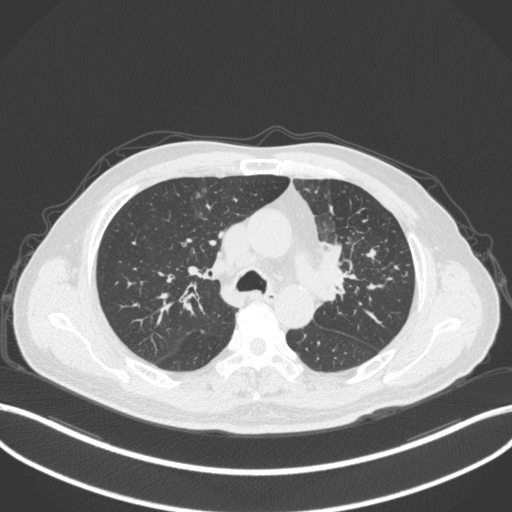
Chest CT, one axial slice. Slice 230 of 386 in the series (ordered by position). Reconstruction kernel B31f. 120 kVp. Lung window (W 1500 / L -600 HU). 1 mm slice thickness. 512 × 512 image matrix, field of view 400 × 400 mm. Patient: male, 69 years. From the clinical record (not read from this slice): clinical TNM (as recorded): T2a N2 M0.
Outlined on this slice (bounding box drawn by a radiologist):
- lung tumour (recorded histology: adenocarcinoma): box from (x=313, y=236) to (x=360, y=297) px